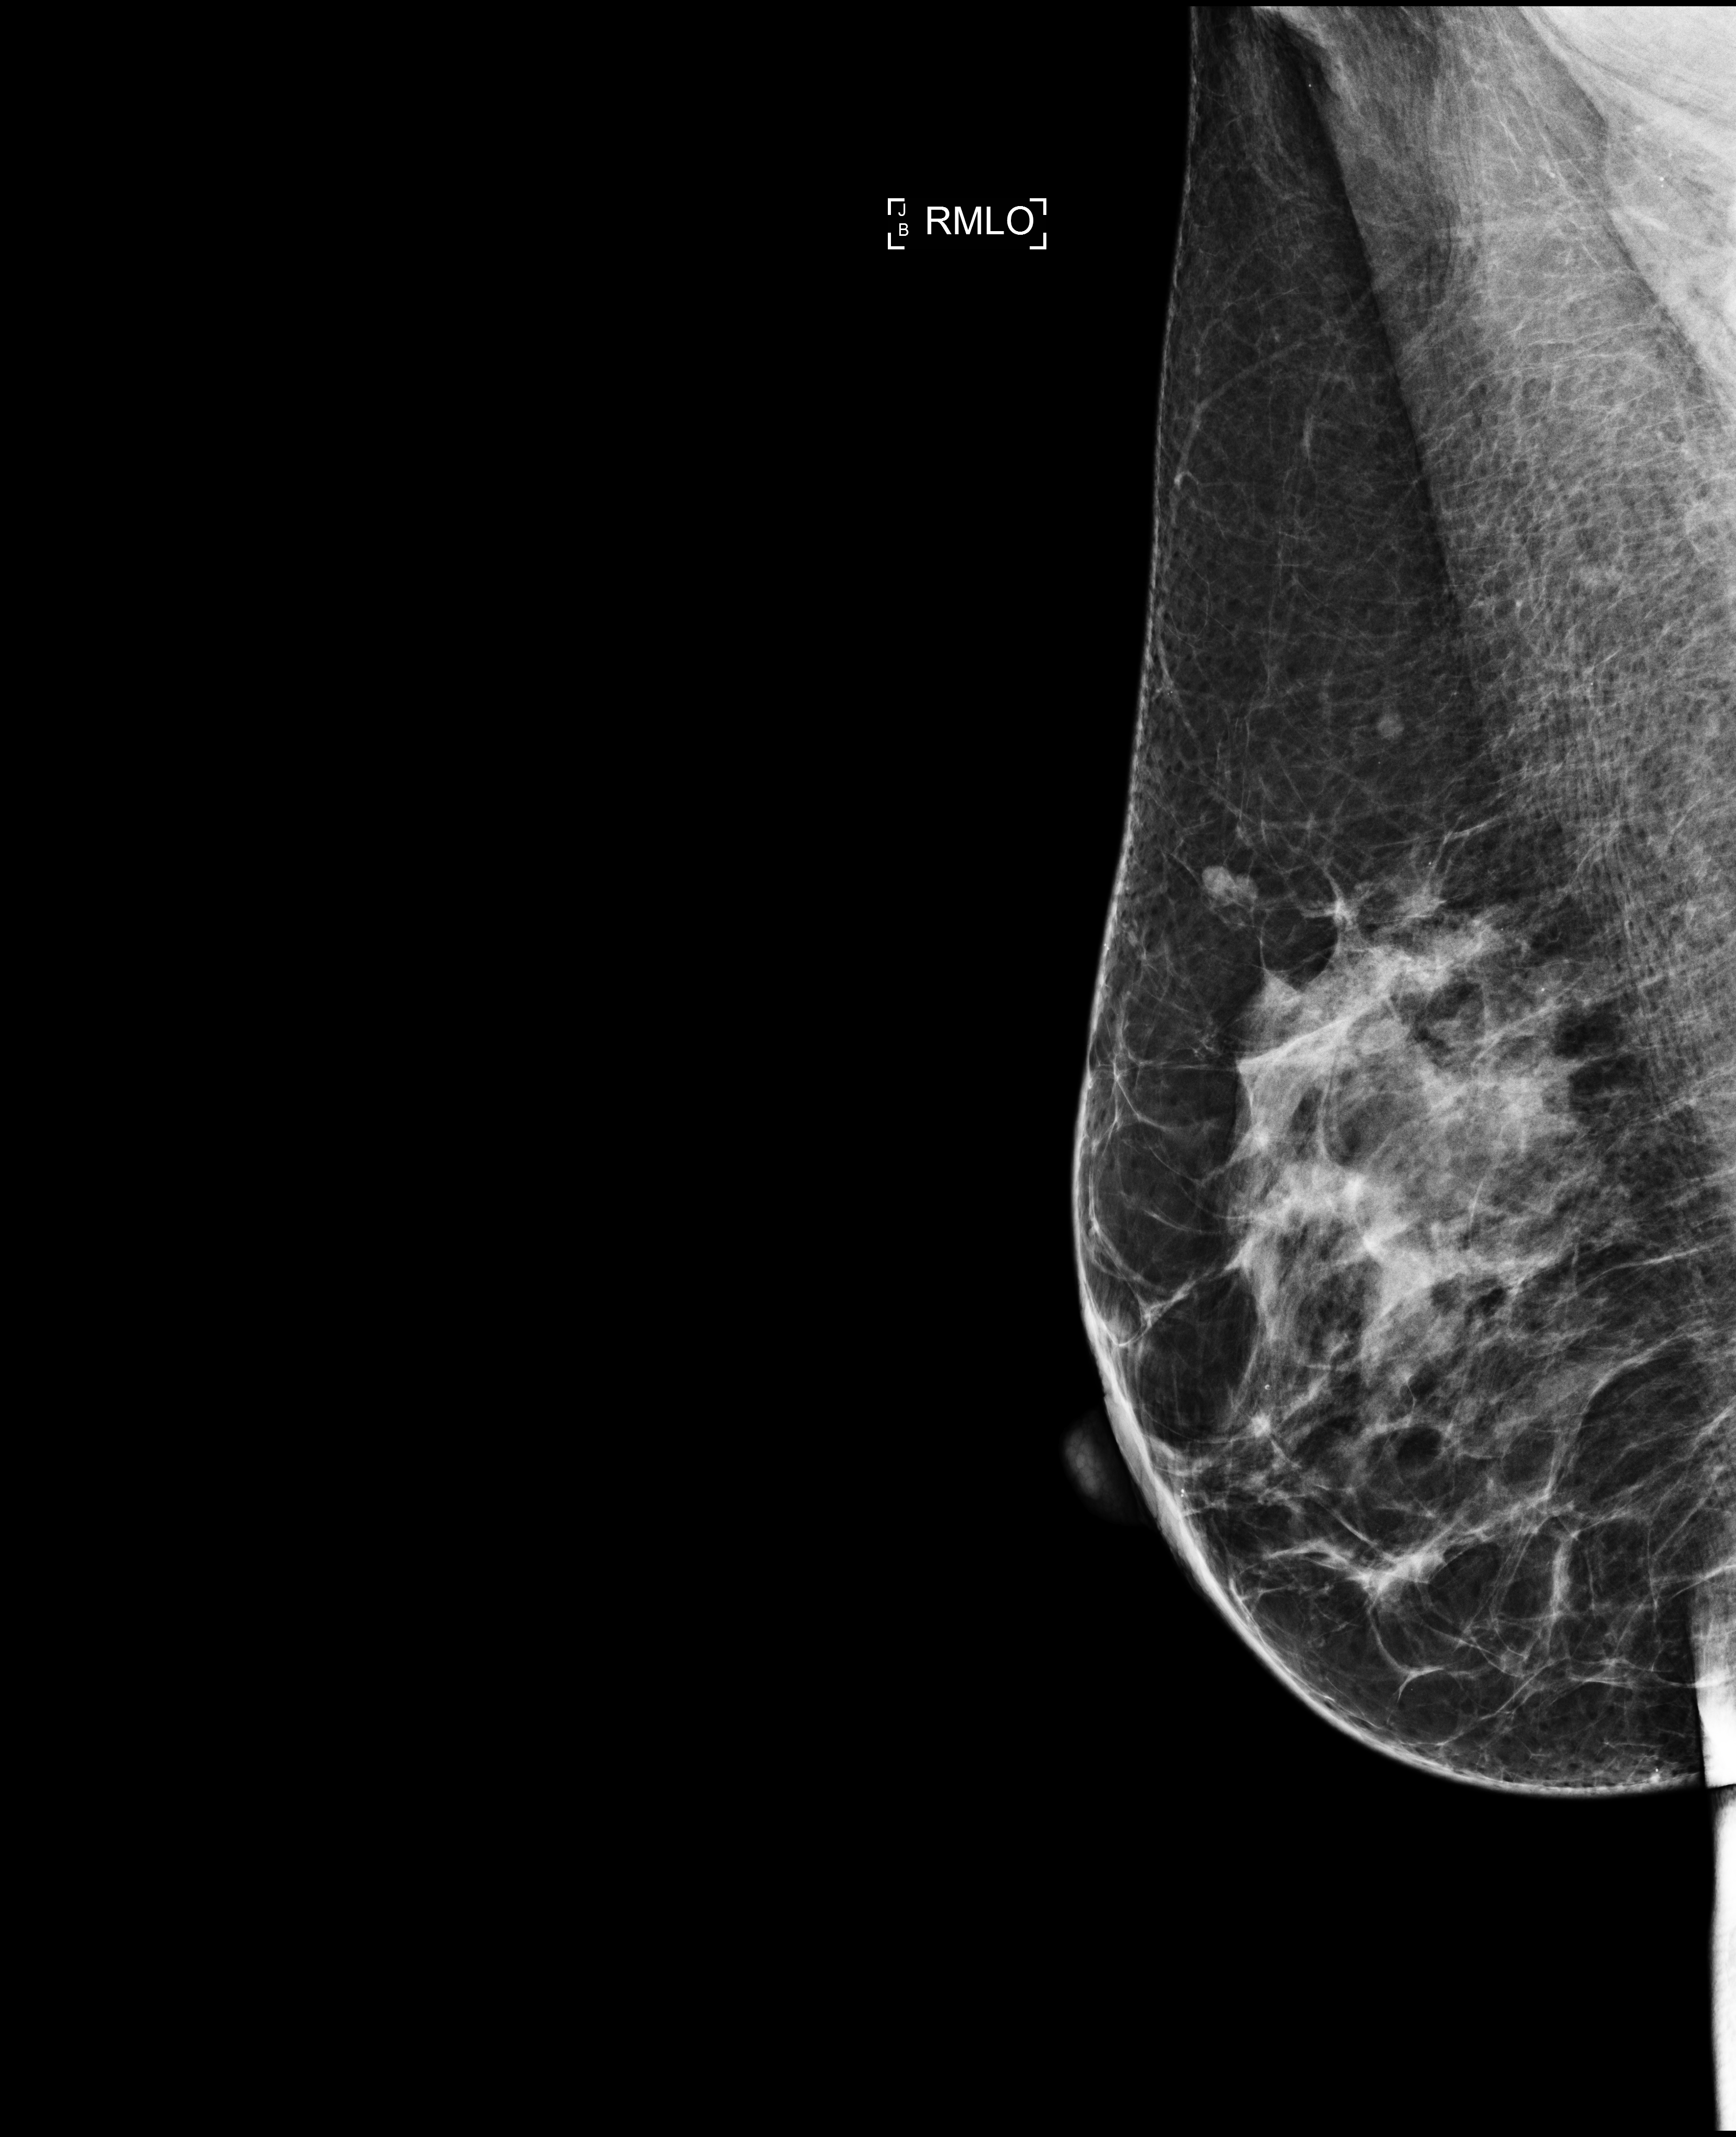
Screening examination; compressed breast thickness 69 mm; system: Selenia Dimensions. Patient: female, 59 years.
Image type: full-field digital mammogram. Breast: right. Projection: mediolateral oblique (MLO) view. Breast density at the screening exam (both breasts): heterogeneously dense (BI-RADS density category c). Final BI-RADS category for the screening round (tomosynthesis exam, both breasts): category 1. Recall: no recall after this screen.